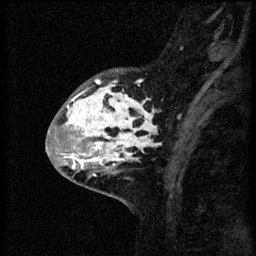
Breast MRI (dynamic contrast-enhanced), one sagittal slice; position 19 of 60 along the scan axis; 3 images stored at this slice position (order not interpretable as contrast timing); 1.5 T; TE 4.2 ms, TR 8.2 ms; 2 mm slice thickness; 256 × 256 image matrix, field of view 180 × 180 mm. Patient: female, 41 years.
Structures marked on this image (semi-automatically segmented with operator editing):
- analysis volume of interest (the breast-tissue region the enhancement analysis was run in; not a lesion): bounding box [x1, y1, x2, y2] px = [53, 70, 159, 175]
- tumour enhancement mask (voxels above the 70 % enhancement threshold inside the analysis volume of interest): [64, 80, 159, 175]